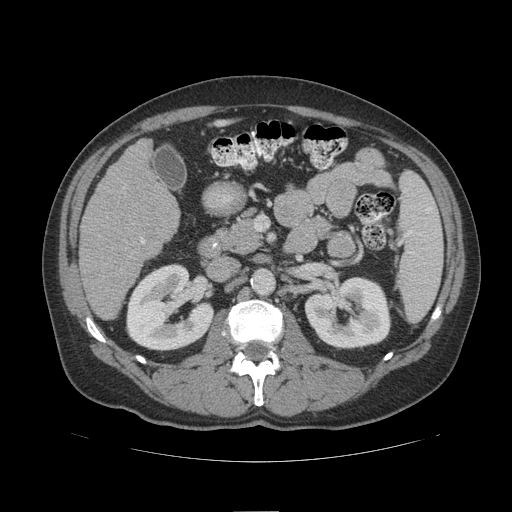
Contrast-enhanced abdominal CT (liver protocol), one axial slice. Position 48 of 109 along the scan axis. Reconstruction kernel STANDARD. 140 kVp. Soft-tissue window (W 400 / L 40 HU). 2.5 mm slice thickness. 512 × 512 image matrix, field of view 420 × 420 mm. Case-level facts recorded for this patient, not image findings: diagnosis: hepatocellular carcinoma (patient treated with transarterial chemoembolisation; whether this scan precedes or follows treatment is not stated here); TNM stage (as recorded): Stage-IIIB; Child-Pugh class: A; tumour differentiation: poorly differentiated; tumour nodularity: multinodular.
Structures marked on this image (semi-automatically segmented with operator editing):
- liver parenchyma outside the tumour (the mass and vessels are separate outlines, so this box may not span the whole liver): bounding box <80,138,180,320> (left, top, right, bottom; pixels)
- liver vessels: <141,240,145,244>